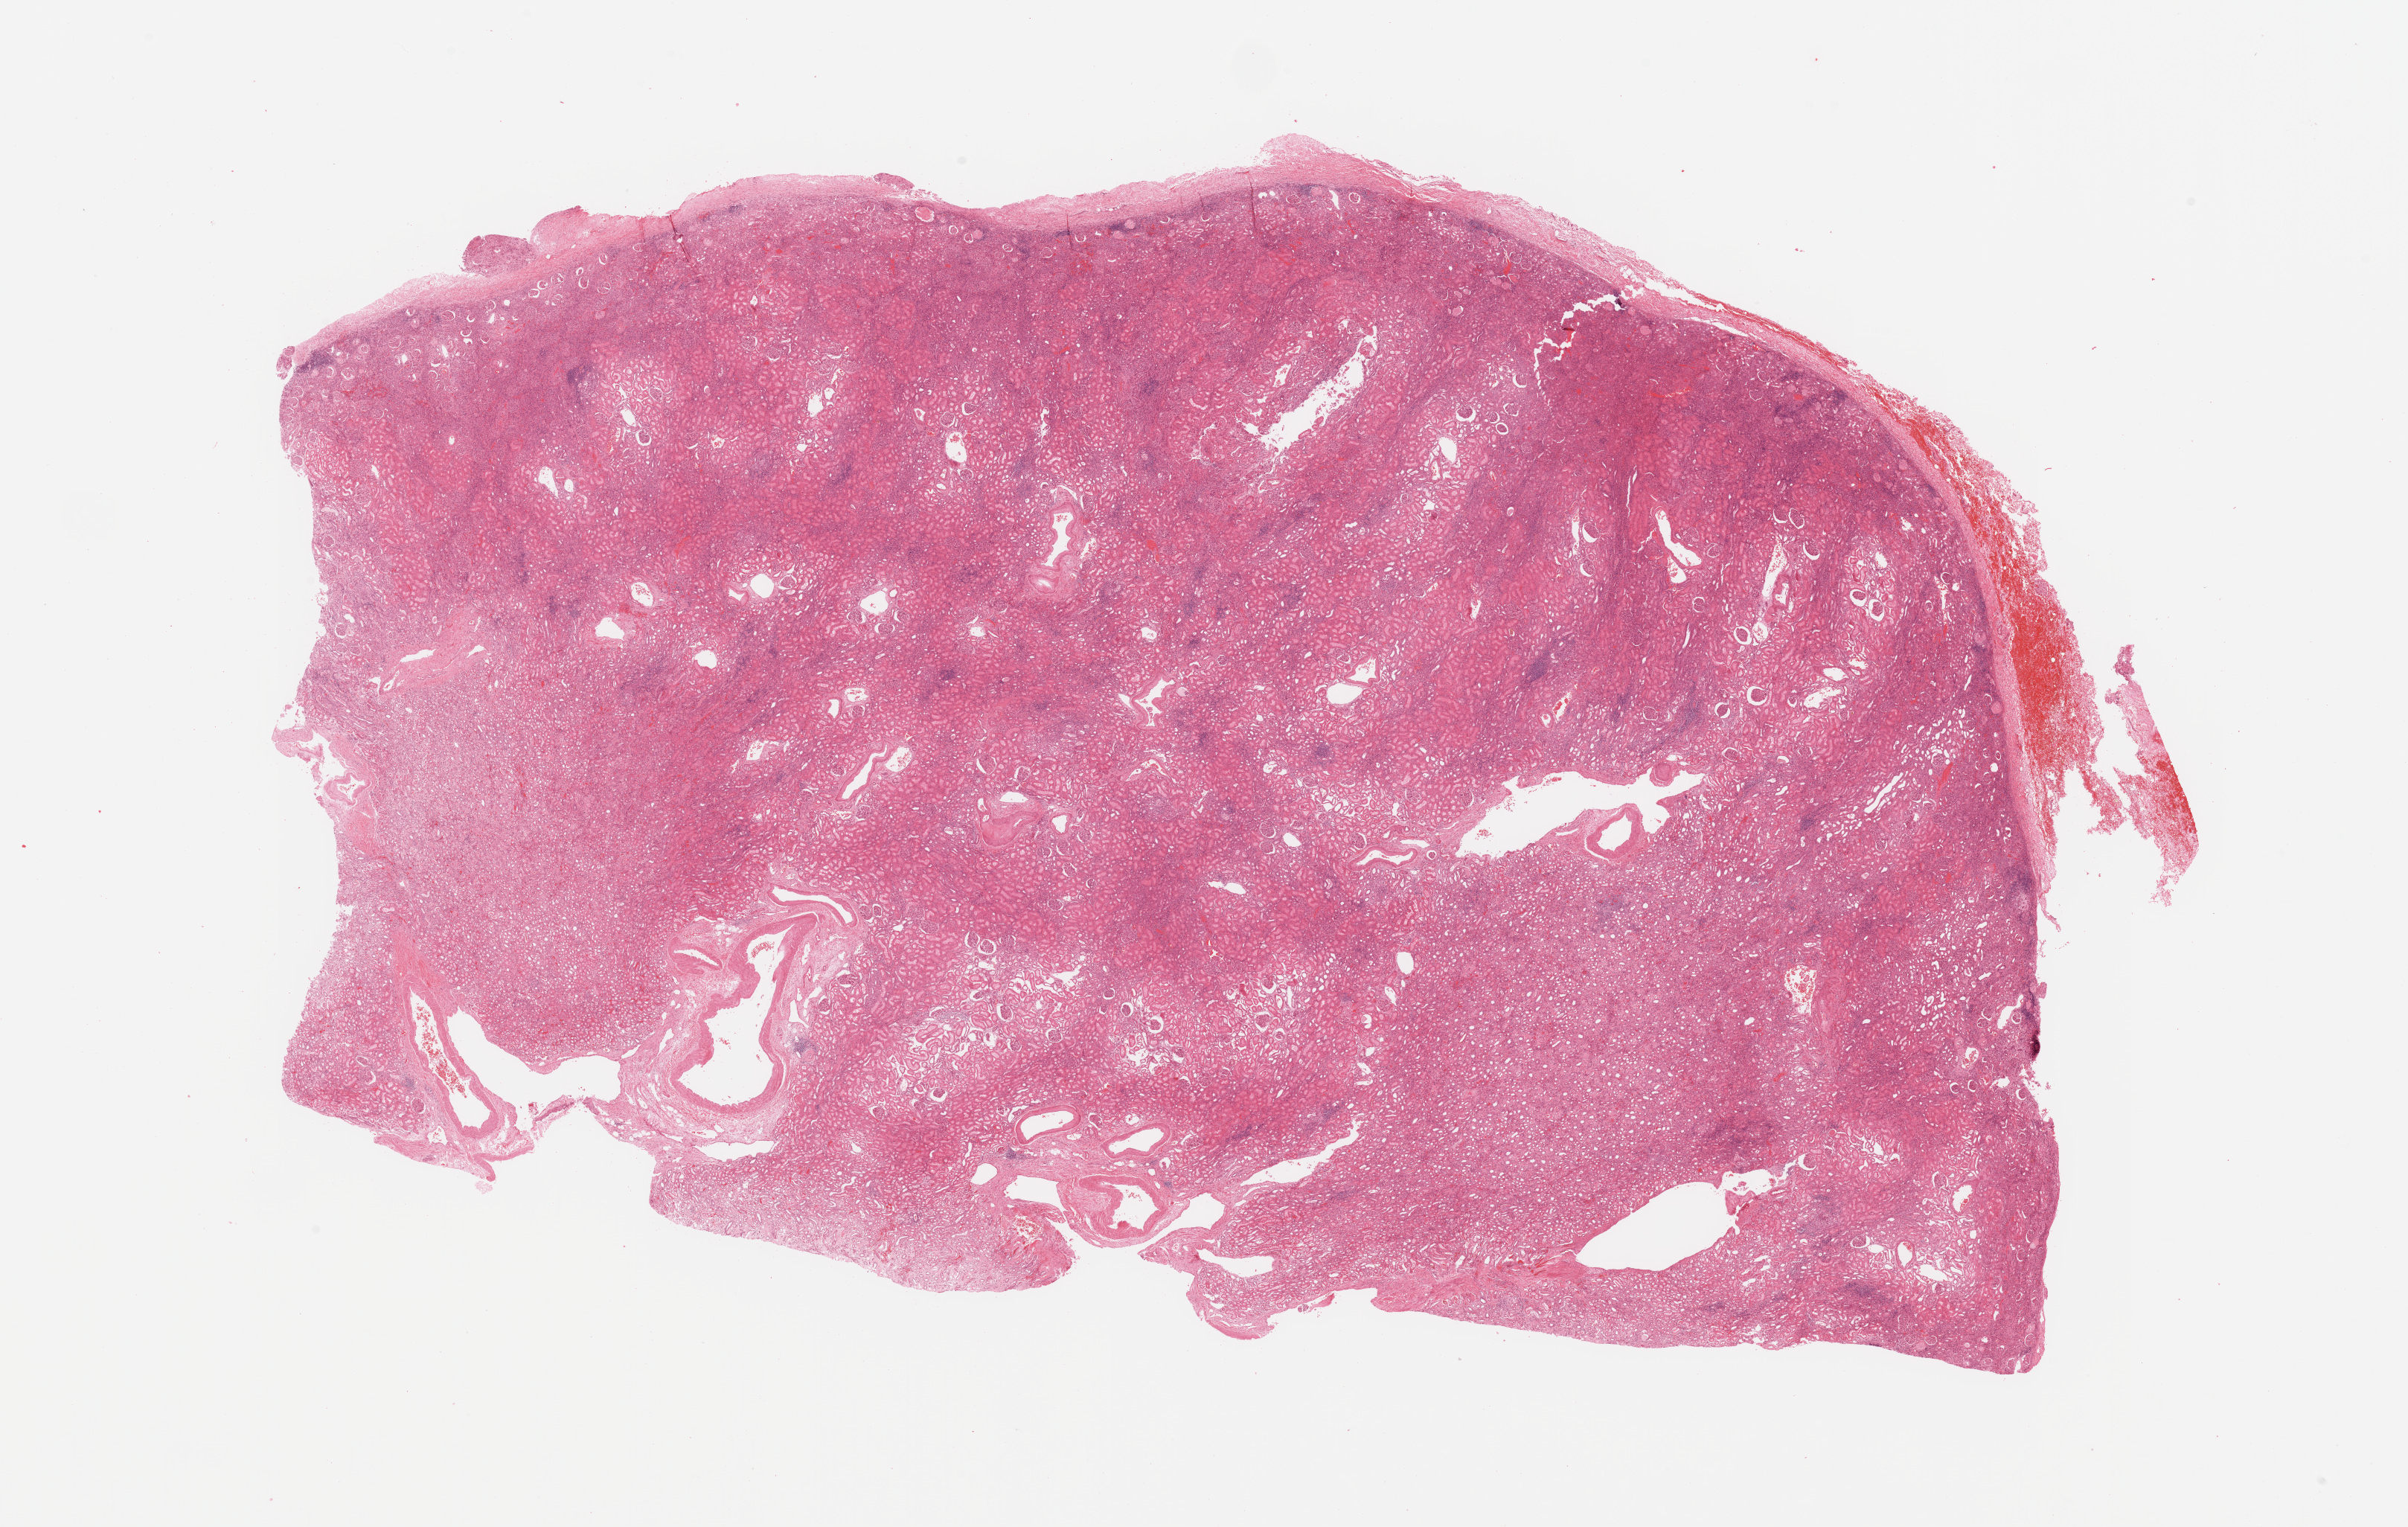
H&E-stained whole-slide image — a low-resolution overview of the entire scanned area, about 25.6 x 16.2 mm (acquisition: 20x scan), normal (non-tumour) tissue sample, sampled site: kidney. Patient: female, age 68 years.
This section: normal (non-tumour) tissue from the same patient. Patient diagnosis: Renal cell carcinoma, NOS.